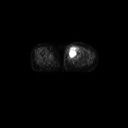
FDG PET of an extremity soft-tissue mass (from a PET/CT study), one axial slice. Slice 42 of 91 in the series (ordered by position). 3.27 mm slice thickness. 128 × 128 image matrix, field of view 700 × 700 mm. Female patient, age 74 years. Case-level facts recorded for this patient, not image findings: histological type: pleomorphic leiomyosarcoma; grade: high; site of the primary tumour: left thigh.
Structures marked on this image (expert contour drawn on MRI and transferred to this co-registered scan by the dataset authors):
- gross tumour volume including surrounding oedema: bounding box (x1, y1, x2, y2) in pixels: (65, 44, 80, 61)
- gross tumour volume (mass): (68, 44, 78, 59)